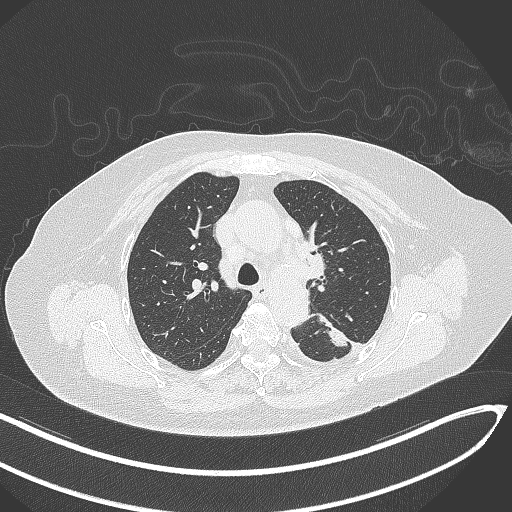
Chest CT, one axial slice; reconstruction kernel B70f; lung window (W 1500 / L -600 HU); 512 × 512 image matrix, field of view 400 × 400 mm. Patient: female, 76 years. Case-level facts recorded for this patient, not image findings: clinical TNM (as recorded): T1c N0 M0.
Annotated regions visible in this slice (rectangle marked by the reading radiologist):
- lung tumour (recorded histology: adenocarcinoma): bounding box <312,312,351,353> (left, top, right, bottom; pixels)